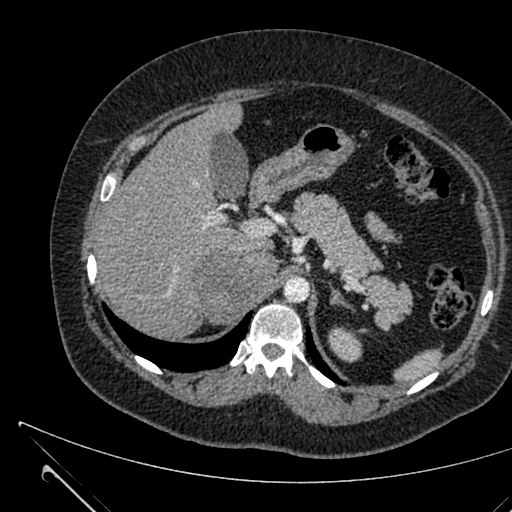
Contrast-enhanced abdominal CT, one axial slice; position 457 of 731 along the scan axis; soft-tissue window (W 400 / L 40 HU); 1 mm slice thickness; 512 × 512 image matrix. Female patient, age 36 years. From the clinical record (not read from this slice): diagnosis: adrenocortical carcinoma; tumour side: right adrenal; tumour size at pathology: 10 cm.
Annotated regions visible in this slice (semi-automatic segmentation, software-assisted and operator-edited):
- mass: bounding box [x1, y1, x2, y2] px = [195, 252, 277, 323]